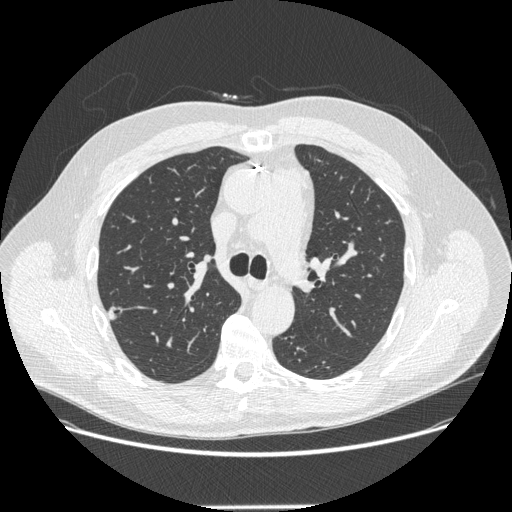
Low-dose screening chest CT, one axial slice. Position 187 of 265 along the scan axis. Reconstruction kernel STANDARD. Lung window (W 1500 / L -600 HU). 1.25 mm slice thickness. 512 × 512 image matrix, field of view 400 × 400 mm.
Structures marked on this image (expert manual segmentation):
- lesion 1 (tumor, upper lobe of right lung): bounding box (x1, y1, x2, y2) in pixels: (107, 306, 122, 320)